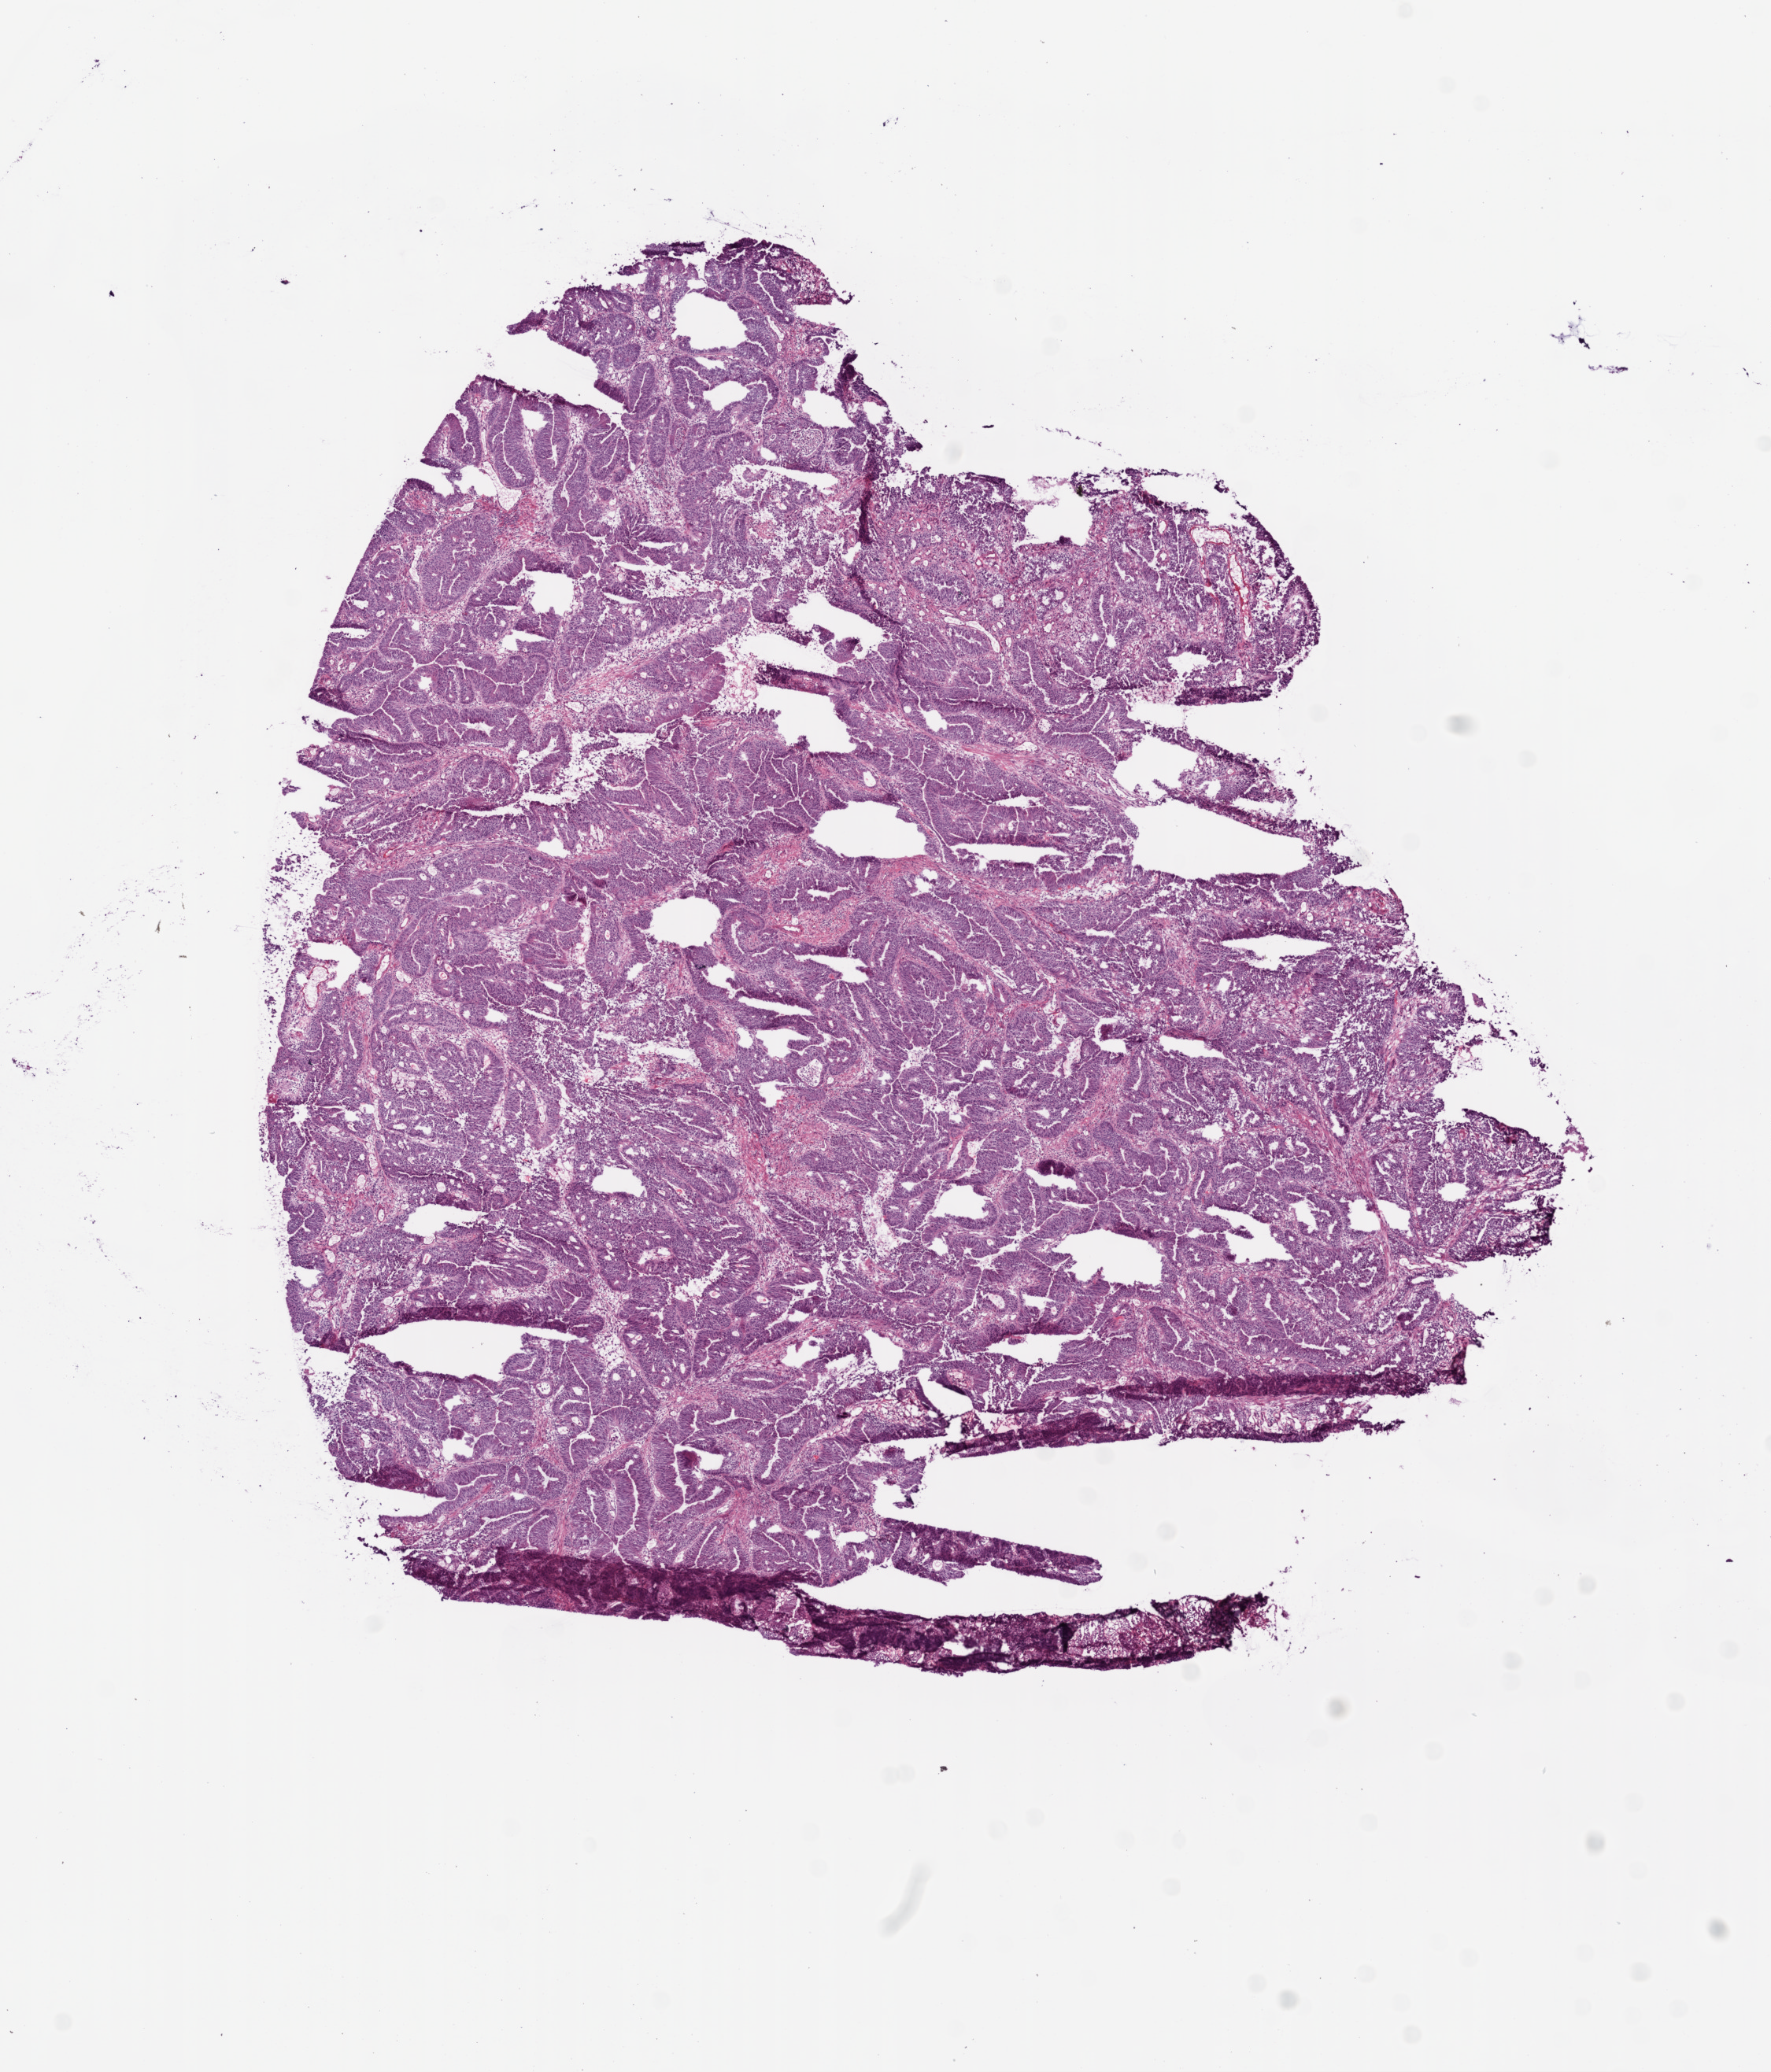
Digitized Hematoxylin and eosin (H&E) stained tissue section (whole slide) — whole scanned area (about 9.0 x 10.6 mm, from a 20x scan) shown as a low-resolution overview. Frozen section from the bottom of the tissue portion. Sample: primary tumour, colon. Male, age 57 years at initial diagnosis. Pathologist review of this section (percent, as recorded): tumour cells 80%, tumour nuclei 90%, normal cells 0%, stromal cells 20%, necrosis 0%. Inflammatory infiltration, as recorded: lymphocyte infiltration 5%.
Lymph nodes positive (case pathology): 0 of 17 examined. Diagnosis: Adenocarcinoma, NOS (sigmoid colon). AJCC pathologic stage: I (6th edition).